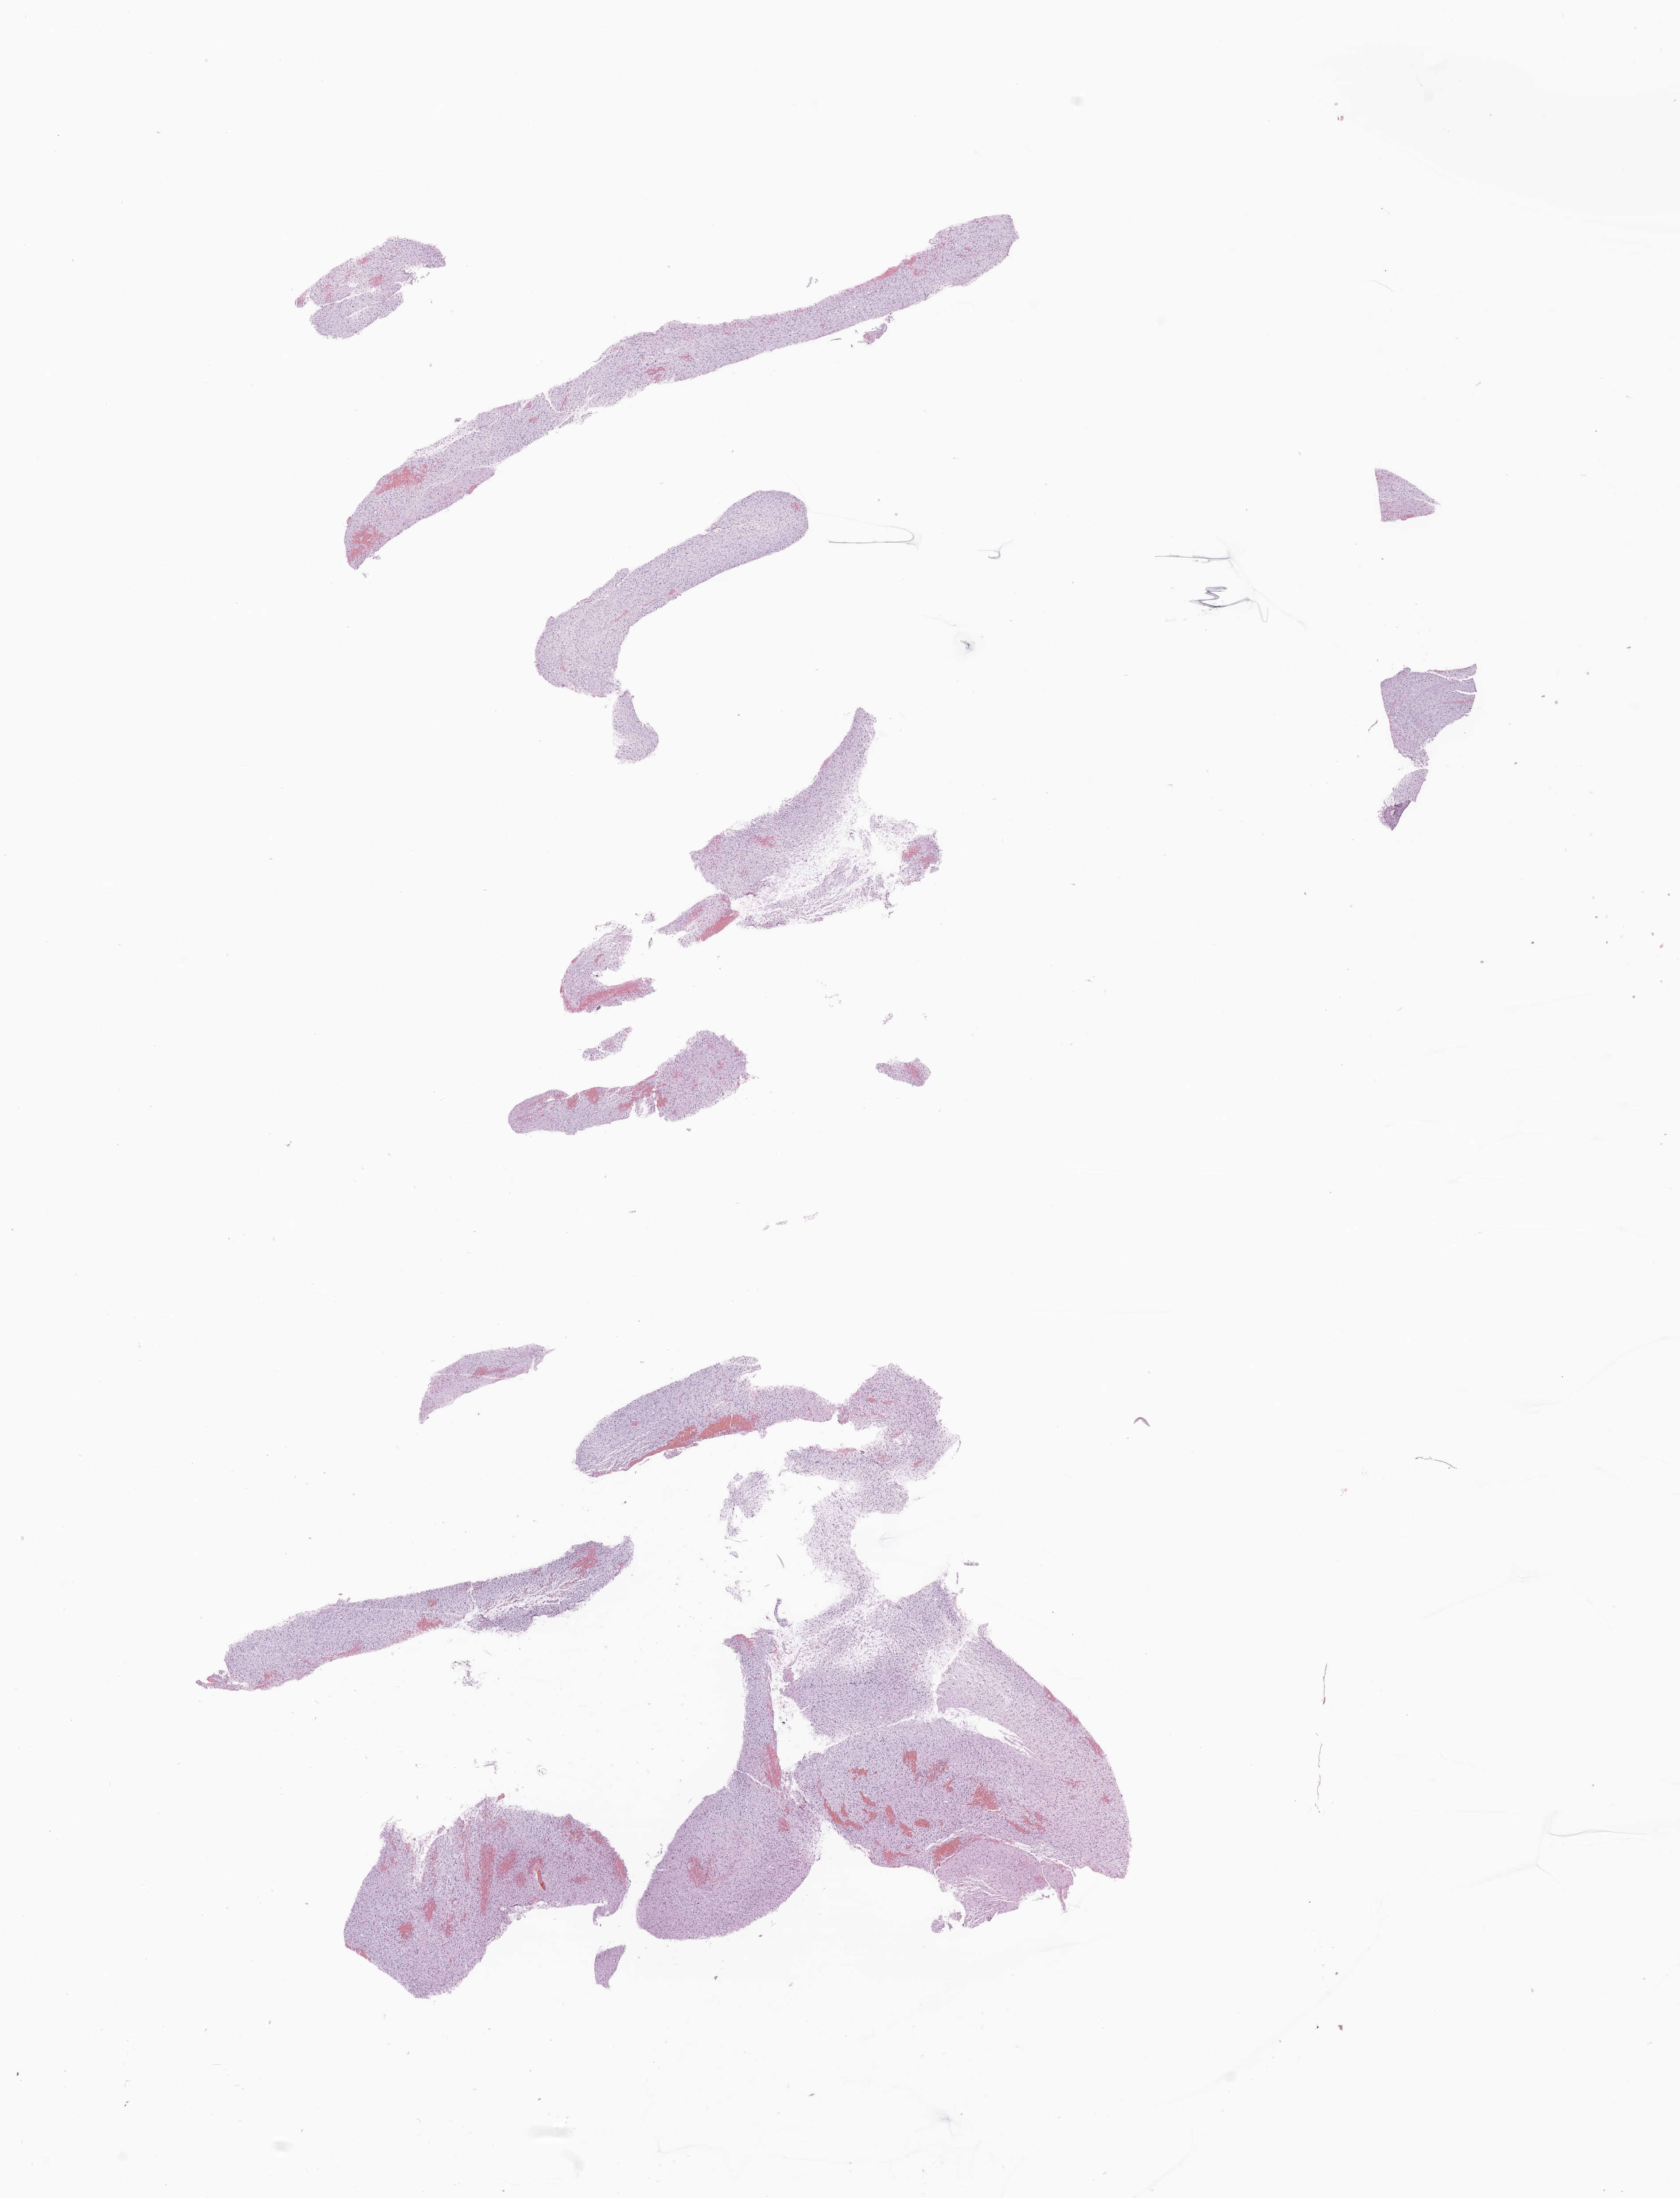
Whole-slide image, H&E stain of tumor tissue from the brain — low-resolution overview of the scanned area, about 16.0 x 20.9 mm; formalin-fixed, paraffin-embedded (FFPE) tissue. Patient female; age 147 months (12 years 3 months).
• diagnosis: Glioma, malignant